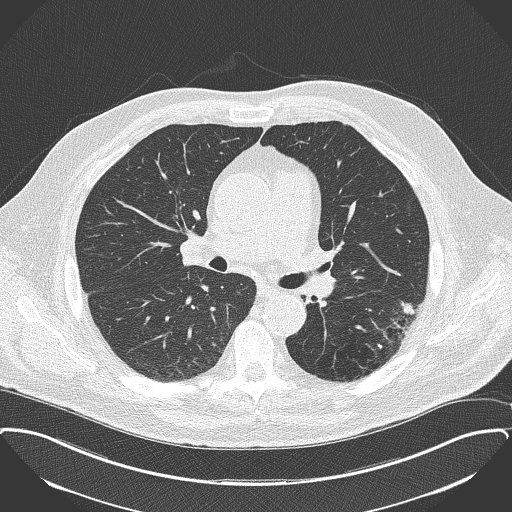
Low-dose screening chest CT, axial slice; second screening round (one year after baseline); lung window (W 1500 / L -600 HU); 2 mm slice thickness; 120 kVp; slice 74 of 175 in the series. Male, age 68 years at enrolment. Former smoker at enrolment.
Lesion marked by an expert reader, box from (x=372, y=293) to (x=429, y=346) px. The screening reader recorded 2 non-calcified nodules or masses ≥4 mm on this exam (left lower lobe, left lower lobe); which of them this box marks is not recorded. Participant outcome: lung cancer diagnosed 126 days after this screen — adenocarcinoma, NOS, left lower lobe, poorly differentiated (G3), stage IB (AJCC 6th edition), 17 mm at pathology.